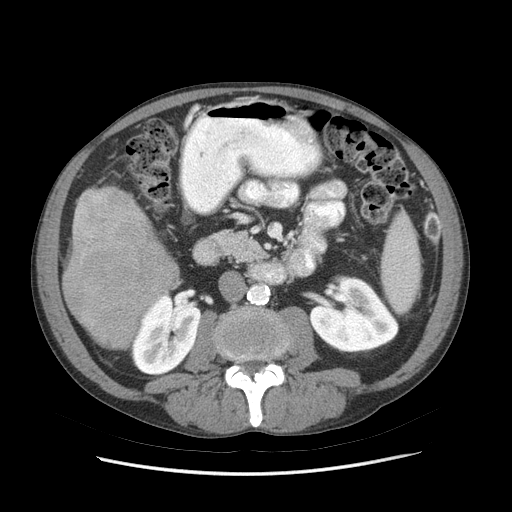
Contrast-enhanced abdominal CT (liver protocol), one axial slice; slice 22 of 89 in the series (ordered by position); reconstruction kernel STANDARD; 140 kVp; soft-tissue window (W 400 / L 40 HU); 2.5 mm slice thickness; 512 × 512 image matrix, field of view 380 × 380 mm. From the clinical record (not read from this slice): diagnosis: hepatocellular carcinoma (patient treated with transarterial chemoembolisation; whether this scan precedes or follows treatment is not stated here); TNM stage (as recorded): Stage-IIIB; Child-Pugh class: A.
Structures marked on this image (semi-automatically segmented with operator editing):
- liver parenchyma outside the tumour (the mass and vessels are separate outlines, so this box may not span the whole liver): box from (x=62, y=186) to (x=180, y=324) px
- mass: (x=63, y=223)–(x=174, y=351)